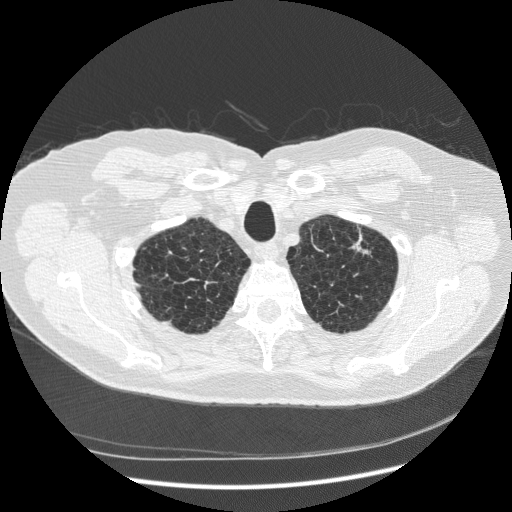
Low-dose screening chest CT, axial slice, baseline screening round, lung window (W 1500 / L -600 HU), 1.25 mm slice thickness, slice 35 of 265 in the series. Male, age 70 years at enrolment. Former smoker at enrolment.
Expert-annotated lung lesion, box from (x=333, y=221) to (x=389, y=277) px. The screening reader recorded 2 non-calcified nodules or masses ≥4 mm on this exam (right lower lobe, right lower lobe); which of them this box marks is not recorded. Participant outcome: lung cancer diagnosed 816 days after this screen (after the third annual screen) — squamous cell carcinoma, NOS, left upper lobe, moderately differentiated (G2), stage IA (AJCC 6th edition), 18 mm at pathology.